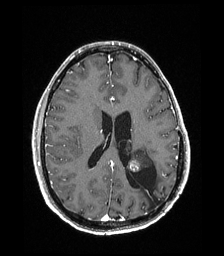
Brain MRI from a brain-tumour surgery series, one axial slice; position 81 of 192 along the scan axis; T1-weighted post-contrast; 1 mm slice thickness; 224 × 256 image matrix. Case-level facts recorded for this patient, not image findings: histopathology: Low grade glioma; IDH mutation: no.
Structures marked on this image (manually delineated by an expert):
- previous resection cavity: box from (x=126, y=165) to (x=162, y=208) px
- tumour: (x=127, y=147)–(x=153, y=172)